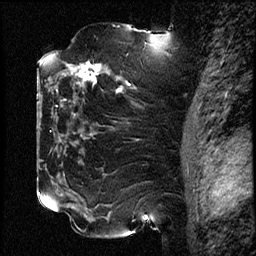
Breast MRI (dynamic contrast-enhanced), one sagittal slice; slice 49 of 78 in the series (ordered by position); dynamic contrast-enhanced study with each time point stored as its own series, time point 2 of 3 at this slice position (early post-contrast, ordered by acquisition time); 1.5 T; TE 4.2 ms, TR 17.6 ms; 2 mm slice thickness; 256 × 256 image matrix, field of view 200 × 200 mm. Patient: female, 42 years. From the clinical record (not read from this slice): setting: breast cancer imaged before/during neoadjuvant chemotherapy; receptor status: HER2-positive.
Outlined on this slice (semi-automatic segmentation, software-assisted and operator-edited):
- analysis volume of interest (the breast-tissue region the enhancement analysis was run in; not a lesion): bounding box (x1, y1, x2, y2) in pixels: (50, 51, 131, 129)
- tumour enhancement mask (voxels above the 100 % enhancement threshold inside the analysis volume of interest): (69, 64, 121, 92)